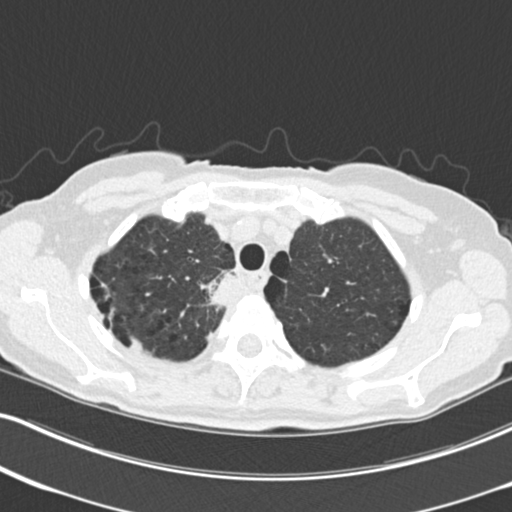
Low-dose screening chest CT, one axial slice. Slice 183 of 226 in the series (ordered by position). Reconstruction kernel B30f. 120 kVp. Lung window (W 1500 / L -600 HU). 2 mm slice thickness. 512 × 512 image matrix.
Outlined on this slice (outlined manually by an expert reader):
- lesion 1 (tumor, mediastinum): bounding box (x1, y1, x2, y2) in pixels: (200, 270, 236, 310)